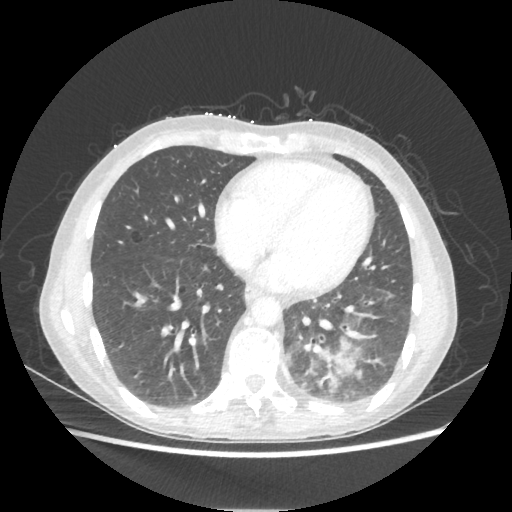
Chest CT, one axial slice; position 83 of 221 along the scan axis; lung window (W 1500 / L -600 HU); 1.25 mm slice thickness; 512 × 512 image matrix, field of view 360 × 360 mm. Patient: female, 53 years. From the clinical record (not read from this slice): clinical TNM (as recorded): T3 N0 M0.
Structures marked on this image (rectangle marked by the reading radiologist):
- lung tumour (recorded histology: adenocarcinoma): bounding box <314,339,355,386> (left, top, right, bottom; pixels)